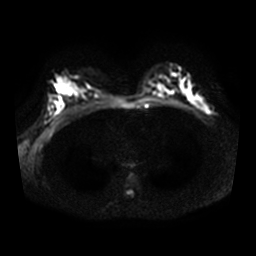
Breast MRI, one axial slice; slice 20 of 32 in the series (ordered by position); diffusion-weighted series; image 2 of 4 stored at this slice position (different b-values; order by instance number); 3 T; 5 mm slice thickness; 256 × 256 image matrix, field of view 340 × 340 mm. Female patient.
Outlined on this slice (expert manual segmentation):
- tumour on diffusion-weighted imaging: bounding box <201,107,208,112> (left, top, right, bottom; pixels)